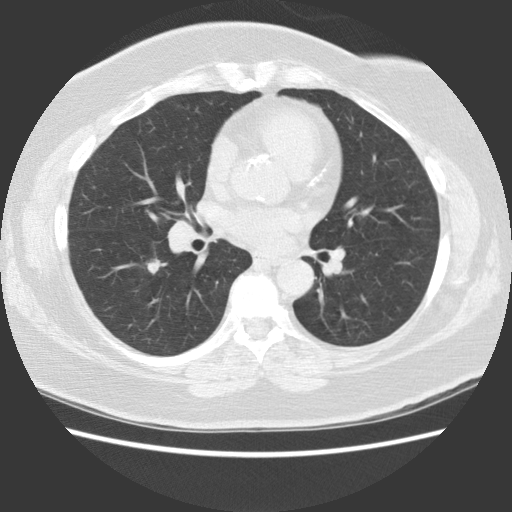
Axial slice from a low-dose chest CT screening exam. Baseline annual screen. Lung window (W 1500 / L -600 HU). 2.5 mm slice thickness. Standard (soft-tissue) reconstruction kernel (STANDARD). Slice 57 of 117 in the series. Female, age 62 years at enrolment.
Expert-annotated lung lesion, box from (x=118, y=239) to (x=179, y=293) px. Reader record for this screening exam (exam-level; its link to the box is not recorded): non-calcified nodule or mass ≥4 mm, right lower lobe, 12 × 10 mm, spiculated (stellate) margins, soft tissue attenuation. Lung cancer was diagnosed 182 days after this screen: large cell carcinoma, NOS, right lower lobe, moderately differentiated (G2), stage IA (AJCC 6th edition), 22 mm at pathology.